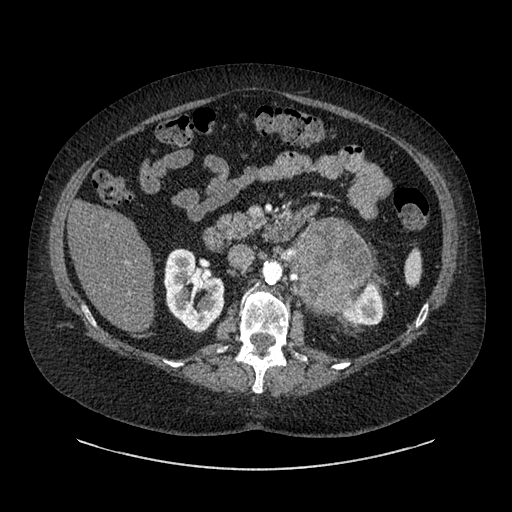
Contrast-enhanced abdominal CT, one axial slice. Slice 523 of 769 in the series (ordered by position). Reconstruction kernel SOFT. Intravenous contrast given. Soft-tissue window (W 400 / L 40 HU). 0.62 mm slice thickness. 512 × 512 image matrix, field of view 460 × 460 mm. Female patient, age 61 years. Case-level facts recorded for this patient, not image findings: diagnosis: adrenocortical carcinoma; tumour side: left adrenal; tumour size at pathology: 13 cm; Ki-67 index: 79 %; stage (as recorded): 2.
Outlined on this slice (semi-automatic segmentation, software-assisted and operator-edited):
- mass: bounding box (x1, y1, x2, y2) in pixels: (293, 220, 375, 307)